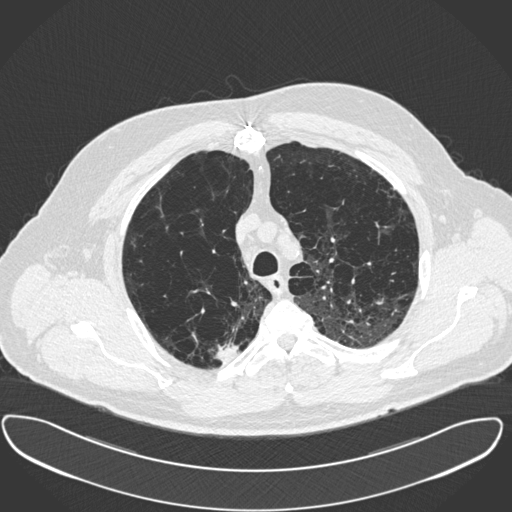
Low-dose screening chest CT, one axial slice. Position 305 of 385 along the scan axis. 120 kVp. Lung window (W 1500 / L -600 HU). 512 × 512 image matrix.
Structures marked on this image (manually delineated by an expert):
- lesion 1 (tumor, upper lobe of right lung): box from (x=214, y=339) to (x=239, y=362) px